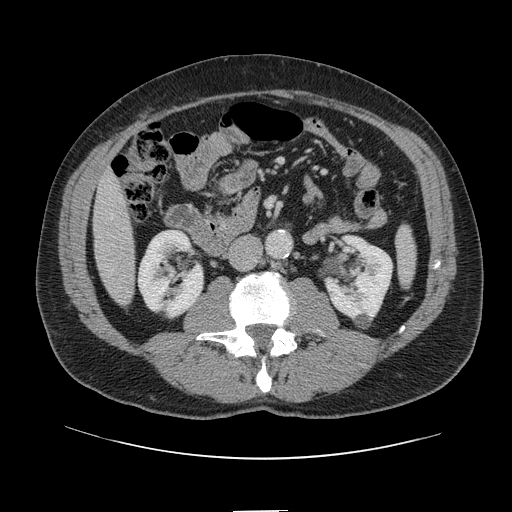
Contrast-enhanced abdominal CT, one axial slice; slice 23 of 161 in the series (ordered by position); intravenous contrast given; soft-tissue window (W 400 / L 40 HU); 2.5 mm slice thickness; 512 × 512 image matrix, field of view 412 × 412 mm. Male patient, age 66 years. Case-level facts recorded for this patient, not image findings: diagnosis: colorectal cancer liver metastases, imaged before liver resection; multiple liver metastases: no; largest metastasis: 3.5 cm.
Structures marked on this image (expert manual segmentation):
- liver: bounding box [x1, y1, x2, y2] px = [94, 172, 134, 304]
- planned liver remnant (the part of the liver to remain after resection): [94, 172, 131, 254]